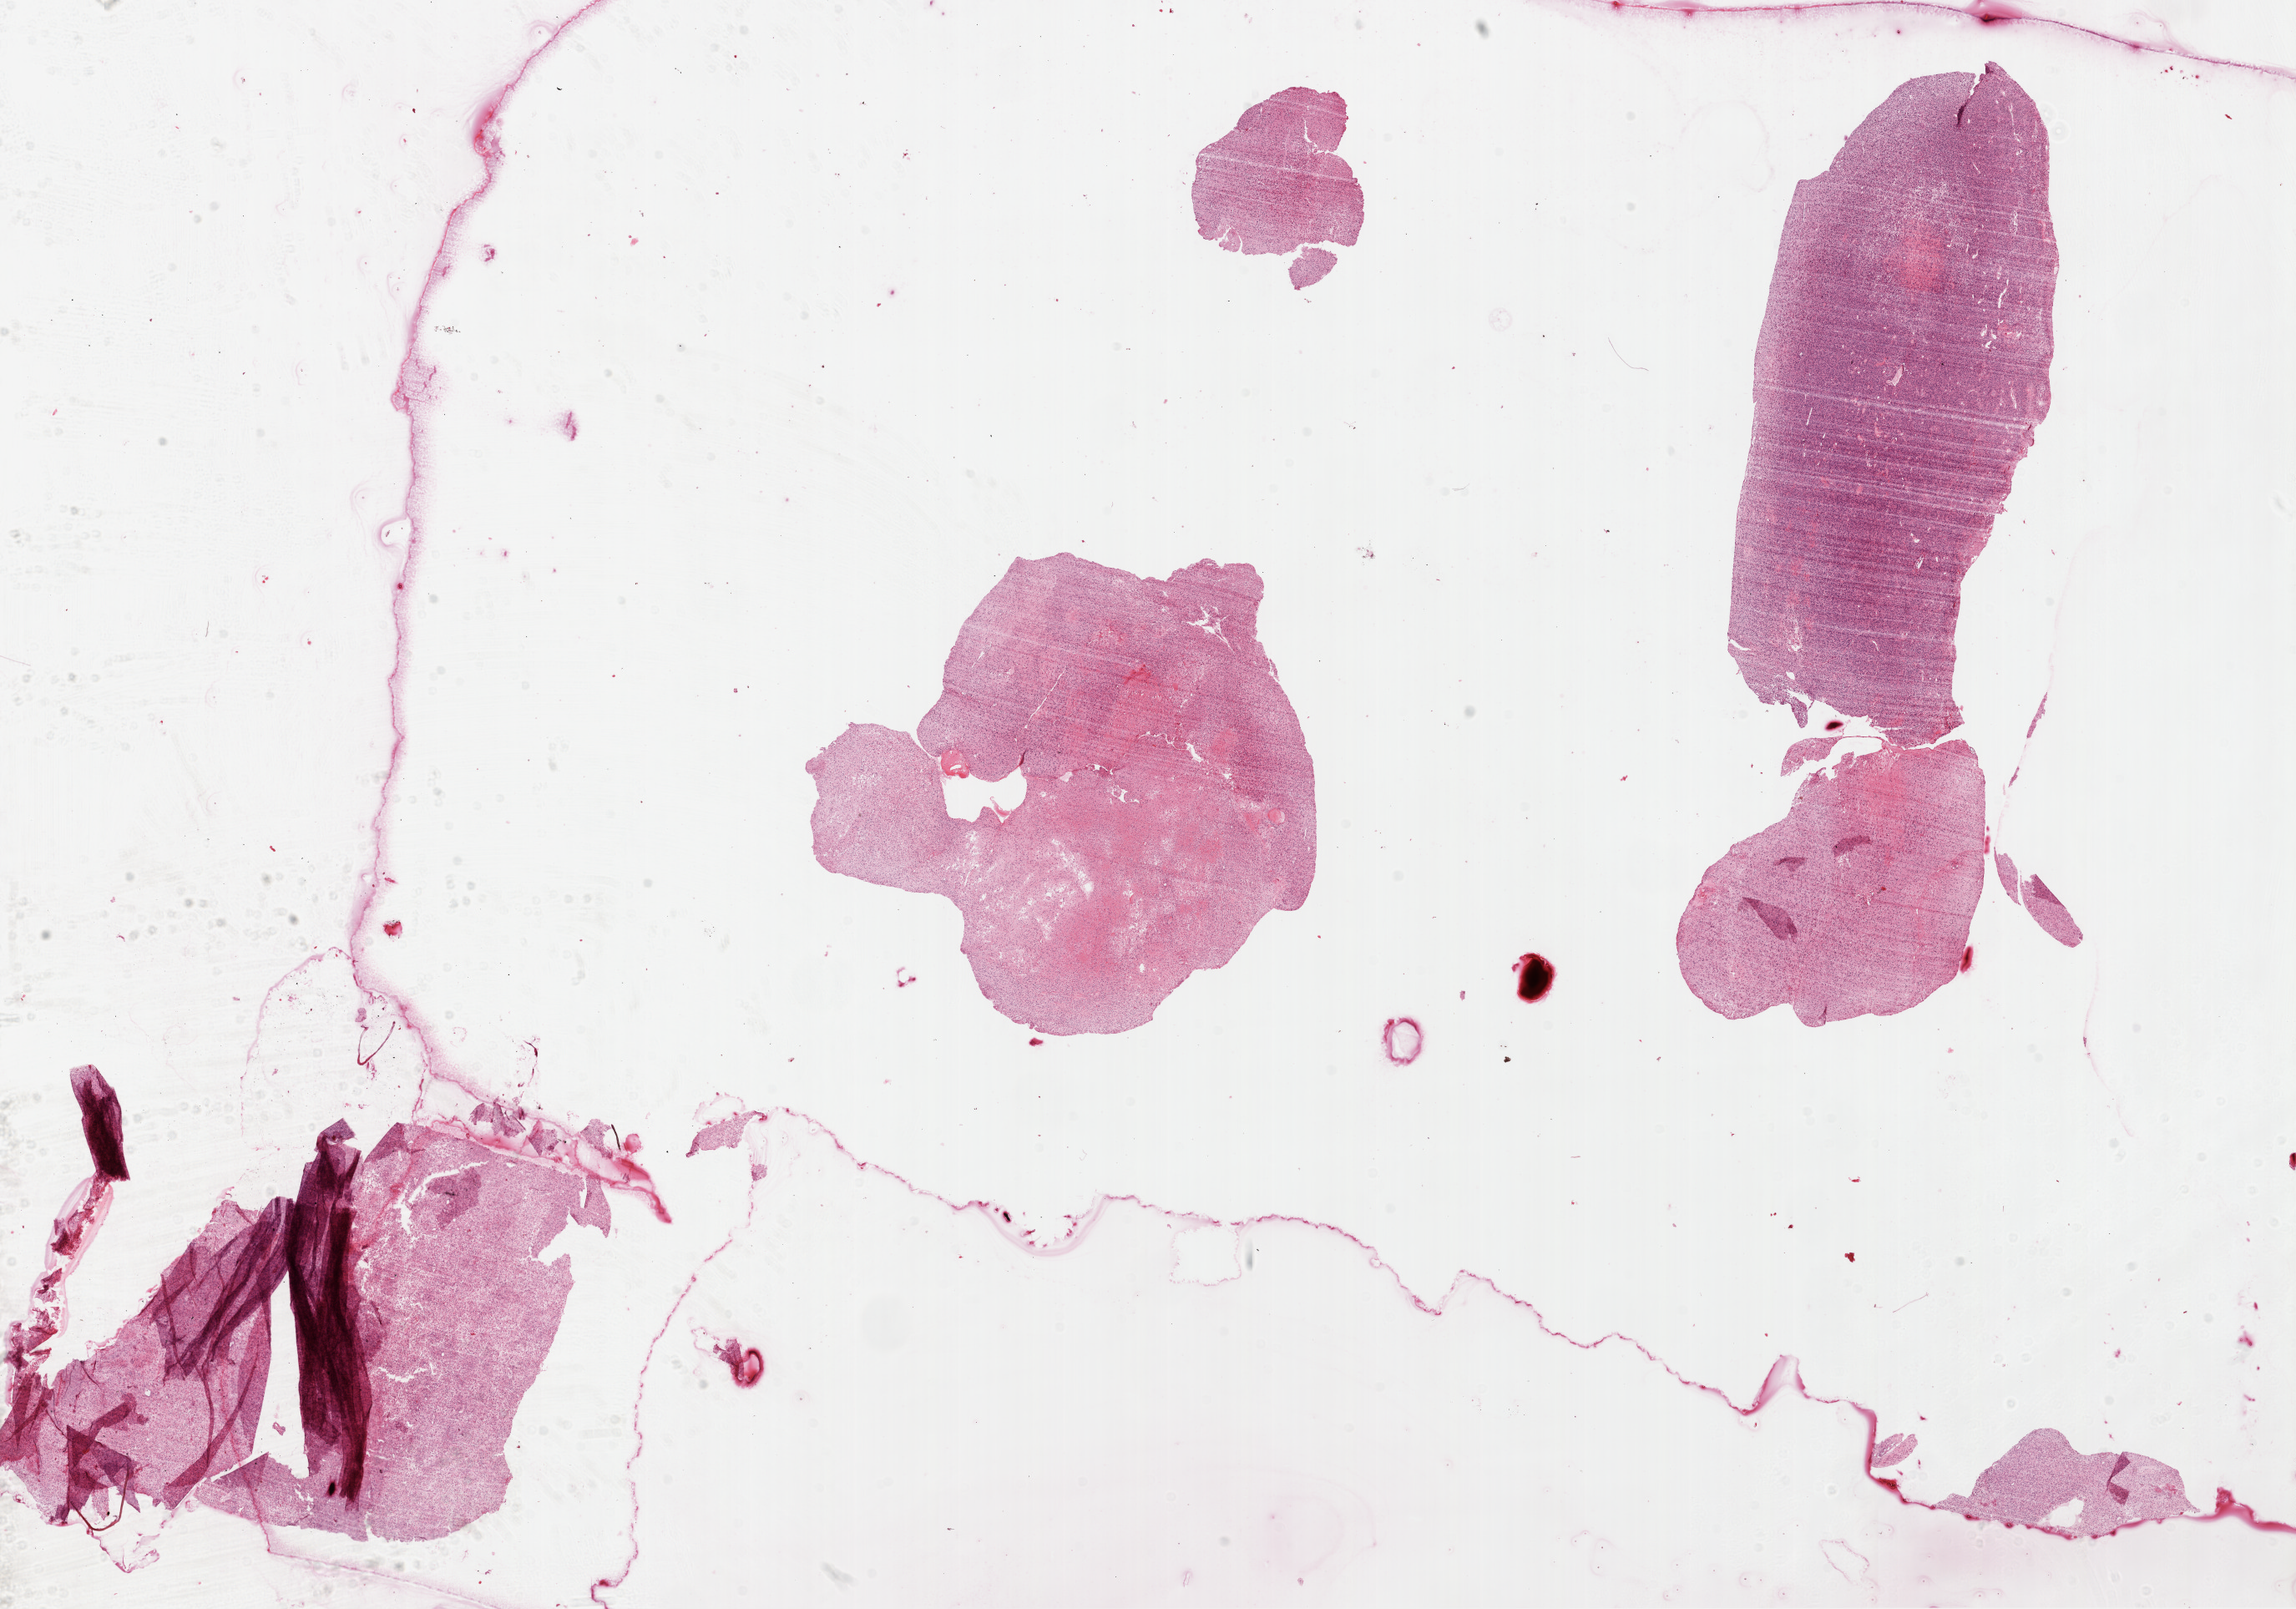
Whole-slide histology image, H&E-stained — whole scanned area (about 22.1 x 15.5 mm, acquisition: 20x scan) shown as a low-resolution overview, formalin-fixed paraffin-embedded (FFPE) diagnostic section, primary tumour sample from the brain. Patient: male, age at initial diagnosis 66 years.
Histologic diagnosis: Glioblastoma.